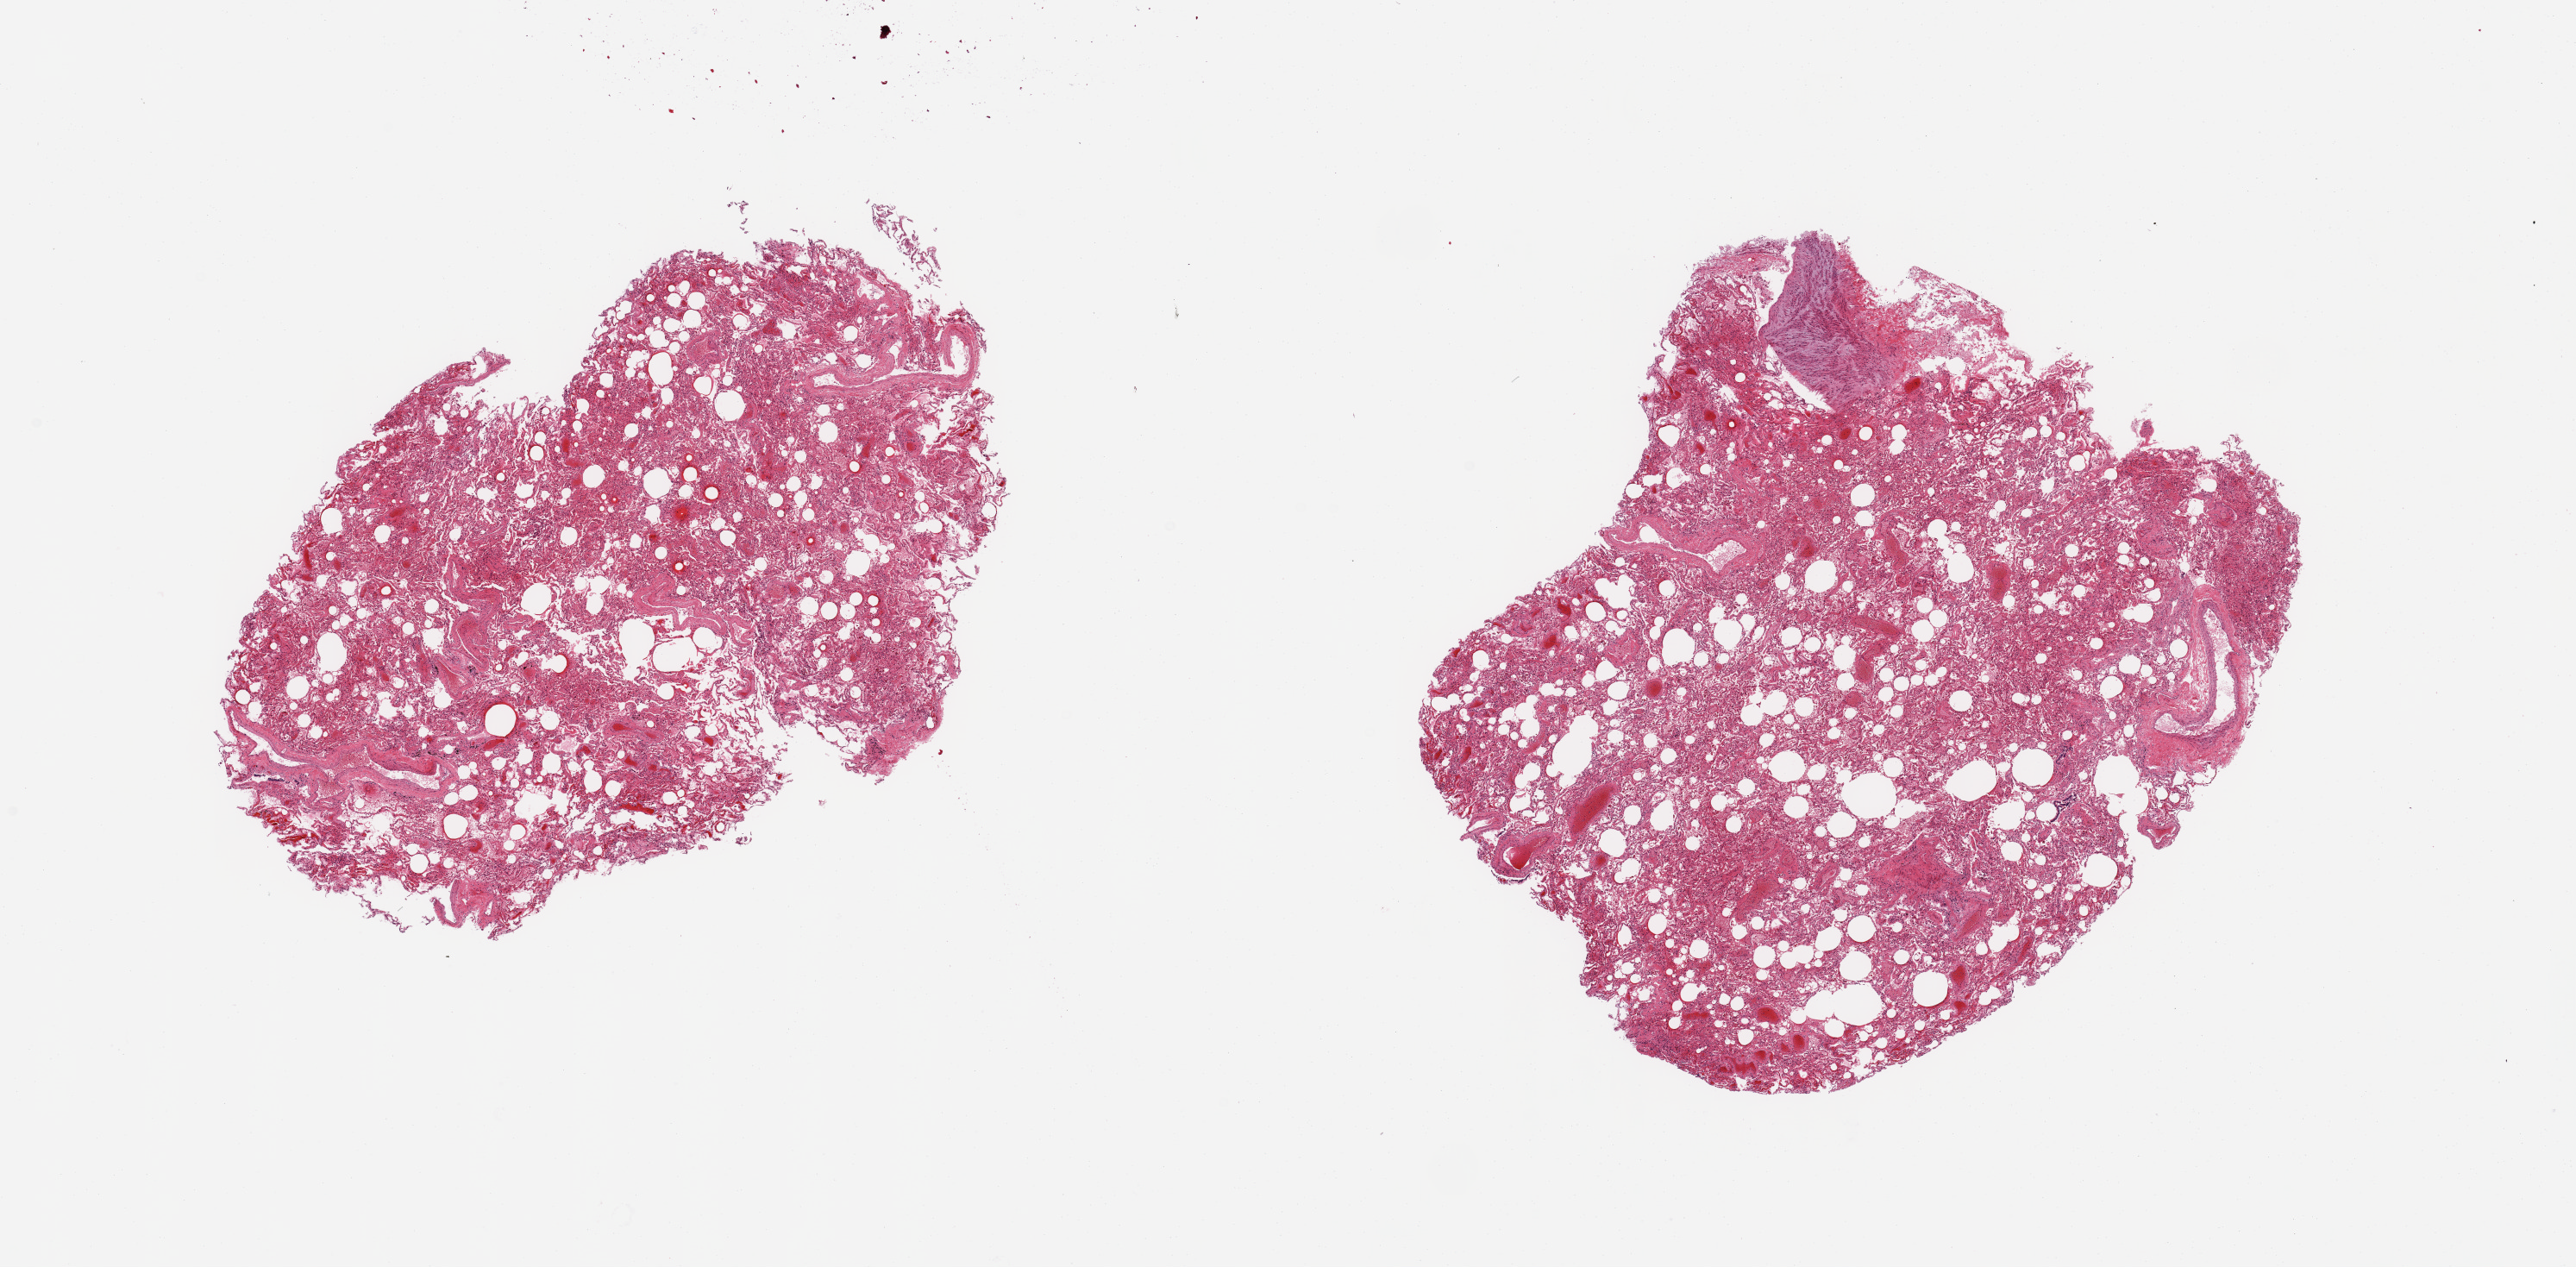
Hematoxylin and eosin (H&E) whole-slide image — whole scanned area (about 23.6 x 11.6 mm, from a 20x scan) shown as a low-resolution overview. PAXgene-fixed, paraffin-embedded tissue. Target tissue: lung. Donor tissue sample. Donor: male.
Pathologist's review note for this sample: 2 pieces; edema, congestion, intra-alveolar macrophages.